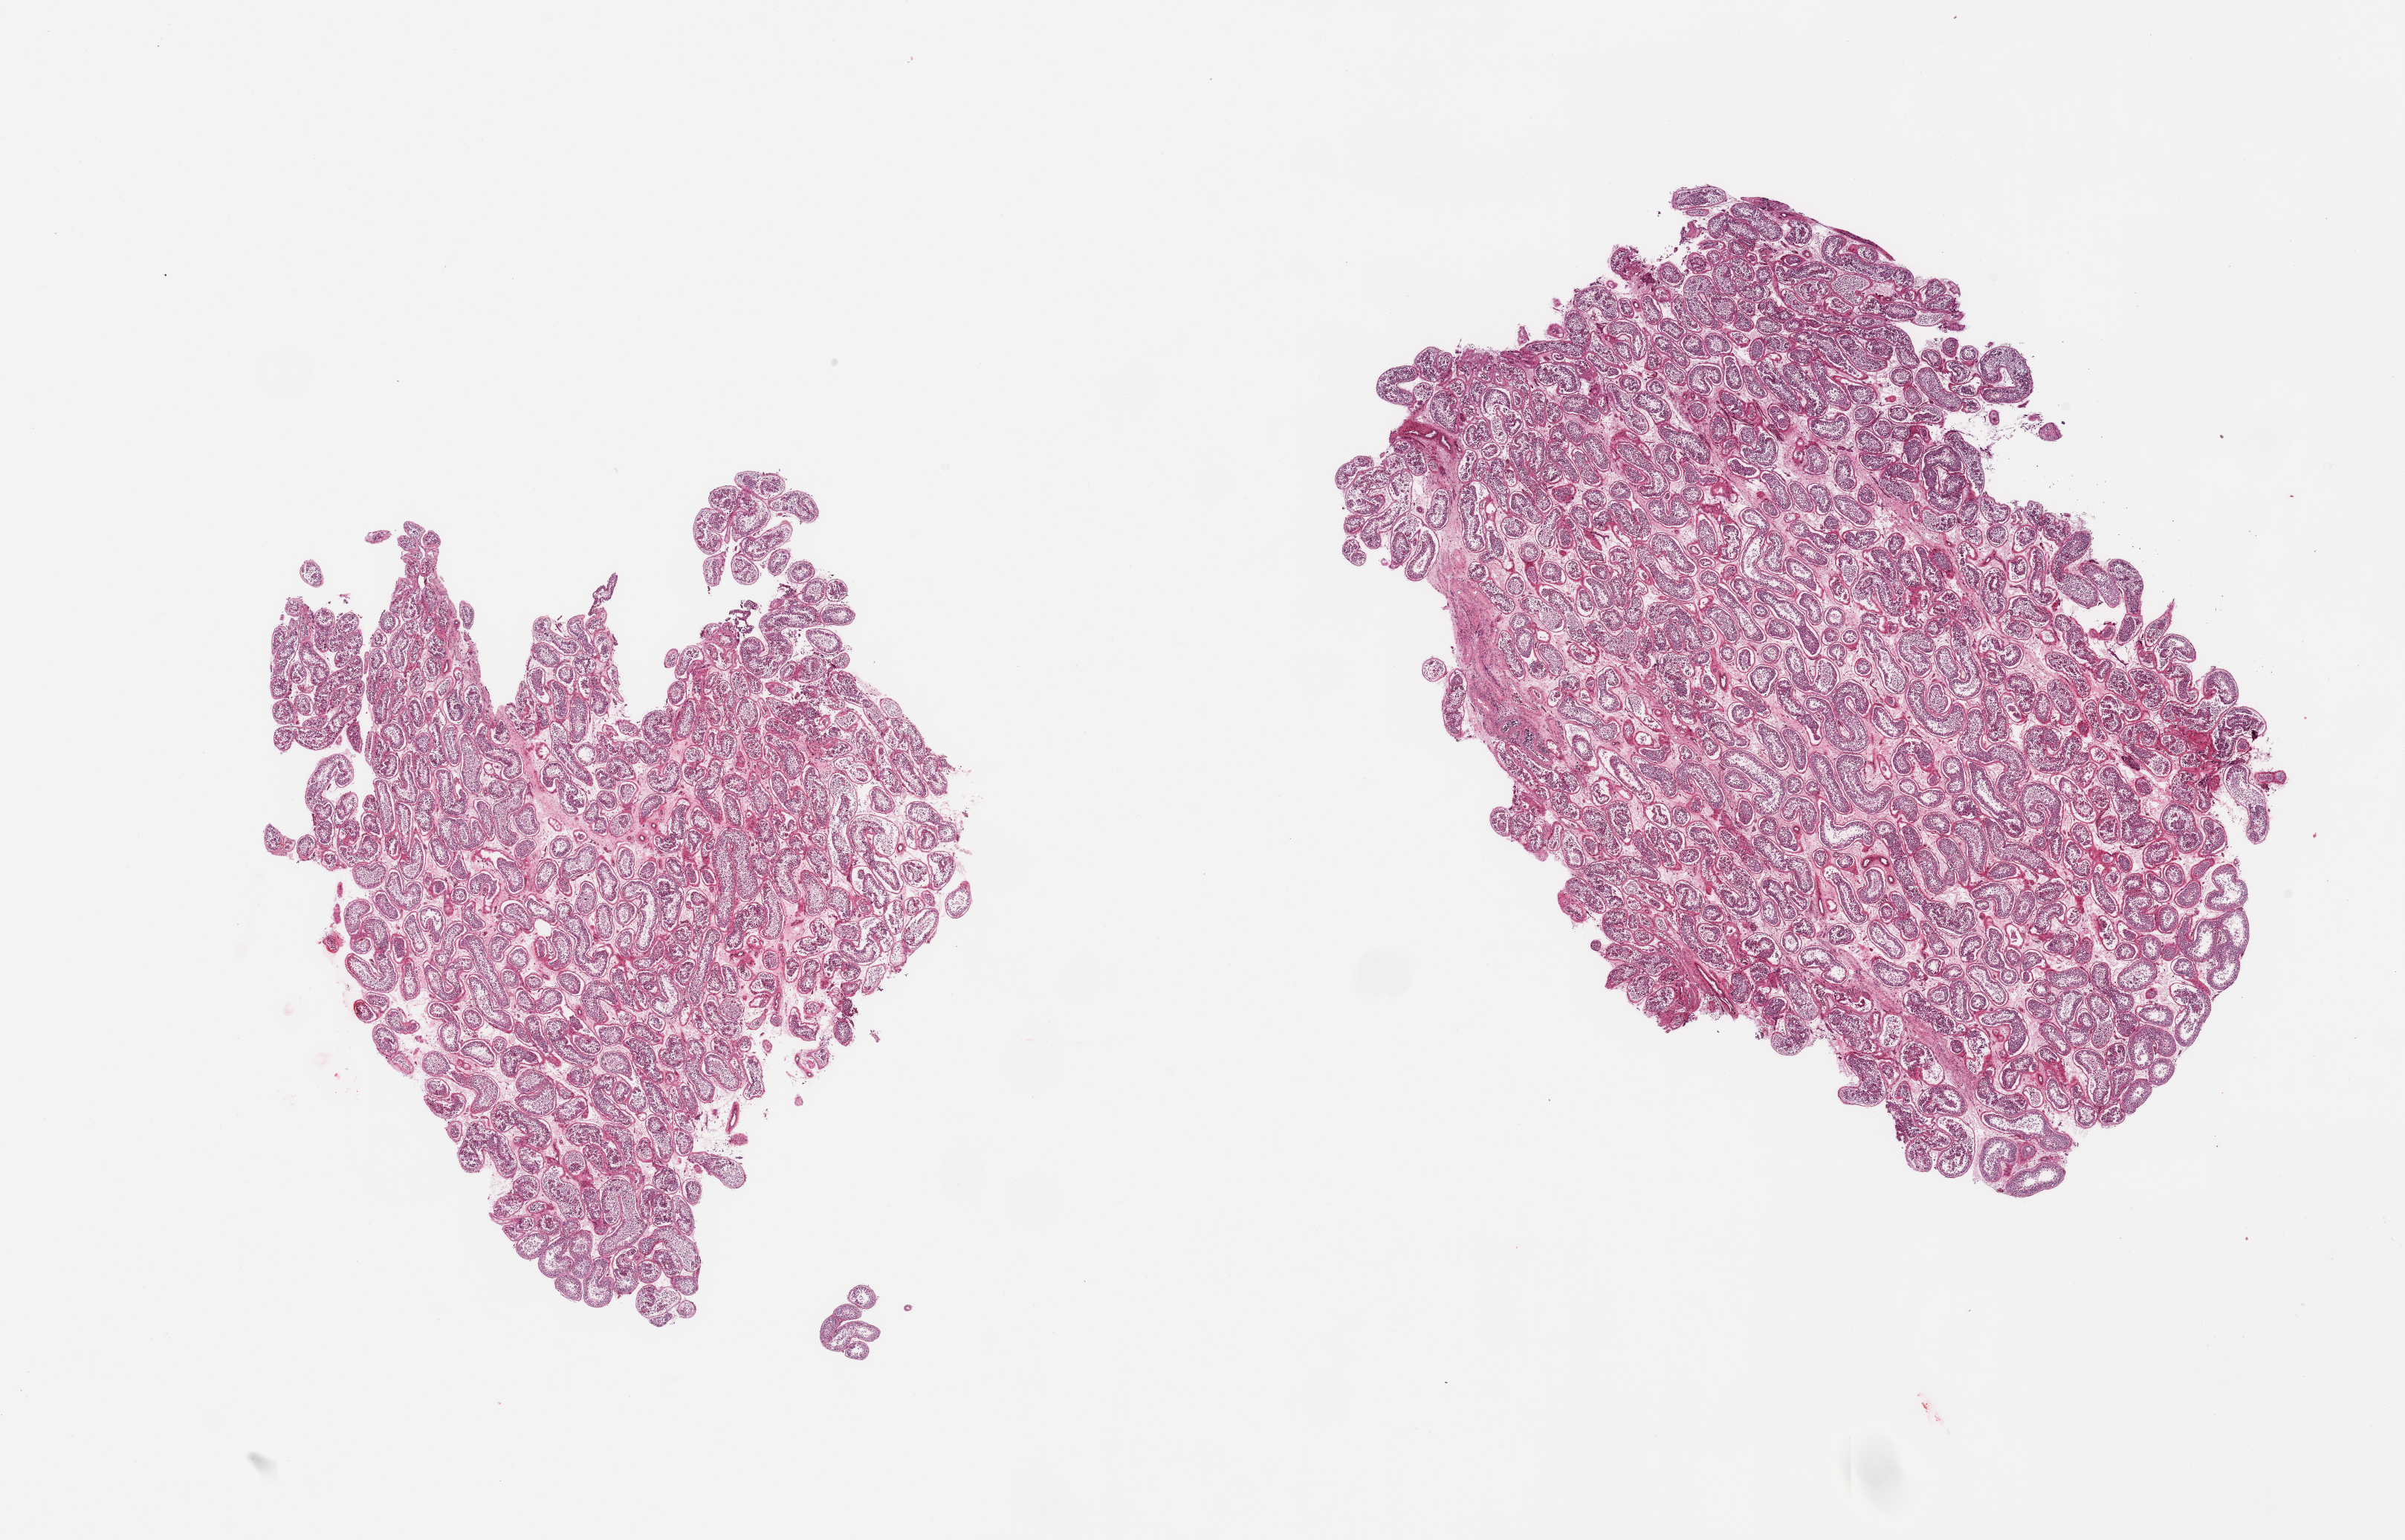
Whole-slide image, hematoxylin and eosin (H&E) stain, low-resolution overview of the scanned area, about 25.6 x 16.4 mm. PAXgene-fixed, paraffin-embedded tissue. Sampled site (target tissue): testis. Donor tissue sample.
Pathologist's review note for this sample: 2 pieces, spermatogenesis present.